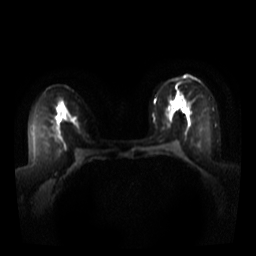
Breast MRI, one axial slice; position 18 of 44 along the scan axis; diffusion-weighted series; image 2 of 4 stored at this slice position (different b-values; order by instance number); 3 T; 5 mm slice thickness; 256 × 256 image matrix, field of view 340 × 340 mm. Female patient.
Annotated regions visible in this slice (expert manual segmentation):
- tumour on diffusion-weighted imaging: bounding box [x1, y1, x2, y2] px = [180, 105, 190, 111]